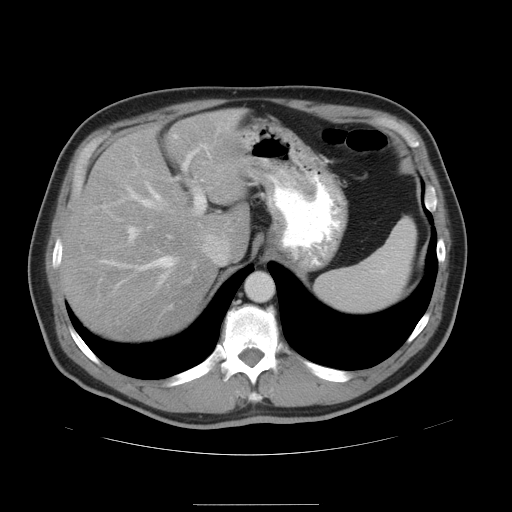
Contrast-enhanced abdominal CT, one axial slice. Slice 35 of 47 in the series (ordered by position). 120 kVp. Intravenous contrast given. Soft-tissue window (W 400 / L 40 HU). 5 mm slice thickness. 512 × 512 image matrix. Male patient, age 61 years. Case-level facts recorded for this patient, not image findings: diagnosis: colorectal cancer liver metastases, imaged before liver resection; multiple liver metastases: no; largest metastasis: 1.2 cm; disease in both lobes: no.
Outlined on this slice (outlined manually by an expert reader):
- hepatic veins: box from (x=101, y=134) to (x=209, y=288) px
- liver: (x=62, y=111)–(x=250, y=342)
- planned liver remnant (the part of the liver to remain after resection): (x=62, y=111)–(x=250, y=342)
- portal vein (with intrahepatic branches): (x=129, y=149)–(x=205, y=287)